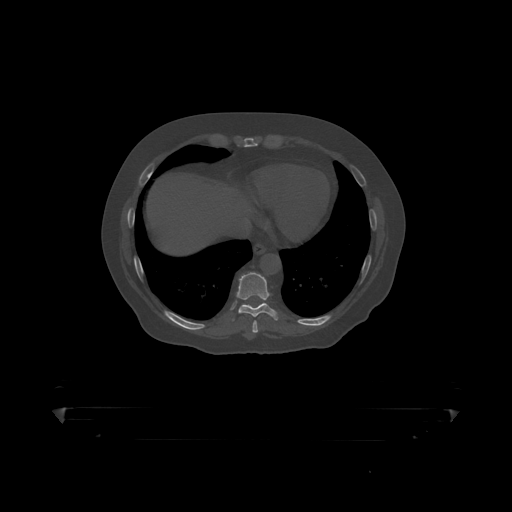
CT including the spine, one axial slice; position 237 of 390 along the scan axis; reconstruction kernel STANDARD; 120 kVp; bone window (W 1800 / L 400 HU); 1.25 mm slice thickness; 512 × 512 image matrix, field of view 650 × 650 mm. Patient: male, 60 years. Case-level facts recorded for this patient, not image findings: primary cancer: prostate.
Structures marked on this image (semi-automatically segmented with operator editing):
- T9 vertebra: bounding box (x1, y1, x2, y2) in pixels: (234, 273, 280, 318)